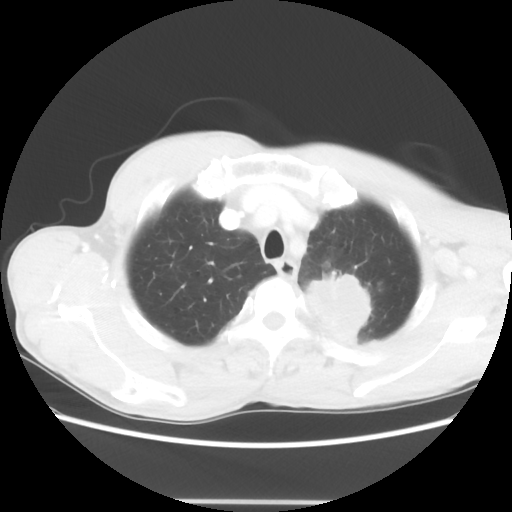
Chest CT, one axial slice; slice 55 of 62 in the series (ordered by position); reconstruction kernel STANDARD; 100 kVp; lung window (W 1500 / L -600 HU); 5 mm slice thickness; 512 × 512 image matrix, field of view 360 × 360 mm. Patient: male, 61 years. From the clinical record (not read from this slice): clinical TNM (as recorded): T3 N1 M1.
Structures marked on this image (rectangle marked by the reading radiologist):
- lung tumour (recorded histology: adenocarcinoma): bounding box [x1, y1, x2, y2] px = [303, 256, 376, 345]